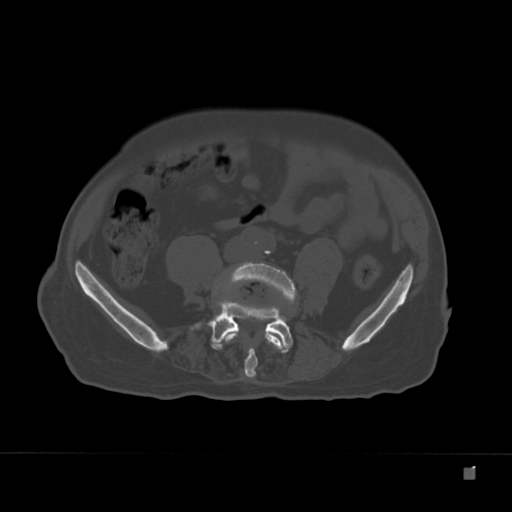
CT including the spine, one axial slice; position 32 of 332 along the scan axis; reconstruction kernel Br40s; 120 kVp; bone window (W 1800 / L 400 HU); 1.5 mm slice thickness; 512 × 512 image matrix, field of view 389 × 389 mm. Male patient, age 72 years. Case-level facts recorded for this patient, not image findings: primary cancer: skeletal.
Structures marked on this image (semi-automatic segmentation, software-assisted and operator-edited):
- L4 vertebra: bounding box <225,262,297,378> (left, top, right, bottom; pixels)
- L5 vertebra: <196,300,293,352>